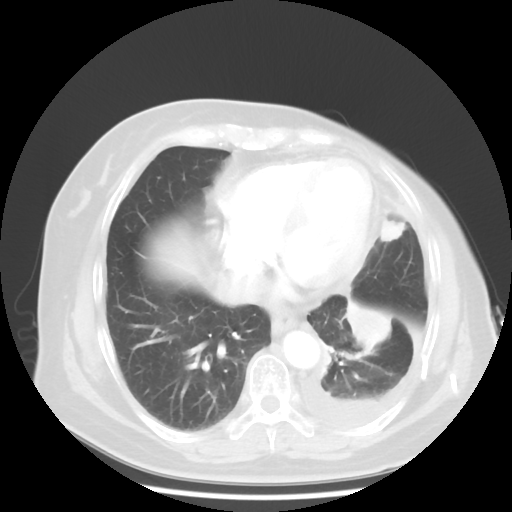
Chest CT, one axial slice; position 15 of 48 along the scan axis; reconstruction kernel STANDARD; lung window (W 1500 / L -600 HU); 5 mm slice thickness; 512 × 512 image matrix, field of view 360 × 360 mm. Female patient, age 63 years. From the clinical record (not read from this slice): clinical TNM (as recorded): T2 N0 M1.
Structures marked on this image (rectangle marked by the reading radiologist):
- lung tumour (recorded histology: adenocarcinoma): bounding box [x1, y1, x2, y2] px = [334, 295, 395, 357]